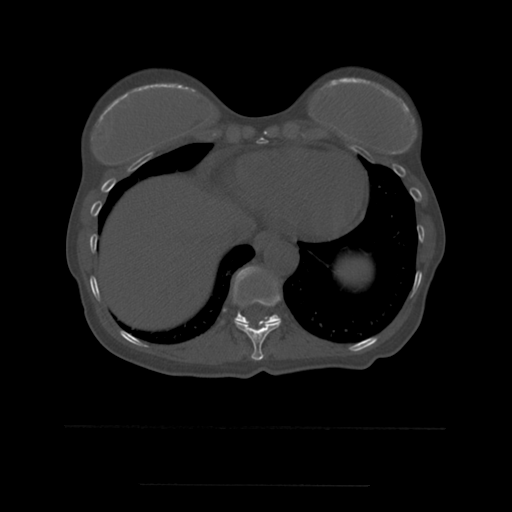
CT including the spine, one axial slice; slice 293 of 544 in the series (ordered by position); bone window (W 1800 / L 400 HU); 512 × 512 image matrix, field of view 350 × 350 mm. Patient age 58 years. Case-level facts recorded for this patient, not image findings: primary cancer: lung.
Outlined on this slice (semi-automatic segmentation, software-assisted and operator-edited):
- T10 vertebra: bounding box (x1, y1, x2, y2) in pixels: (235, 281, 282, 361)
- T11 vertebra: (224, 267, 281, 323)